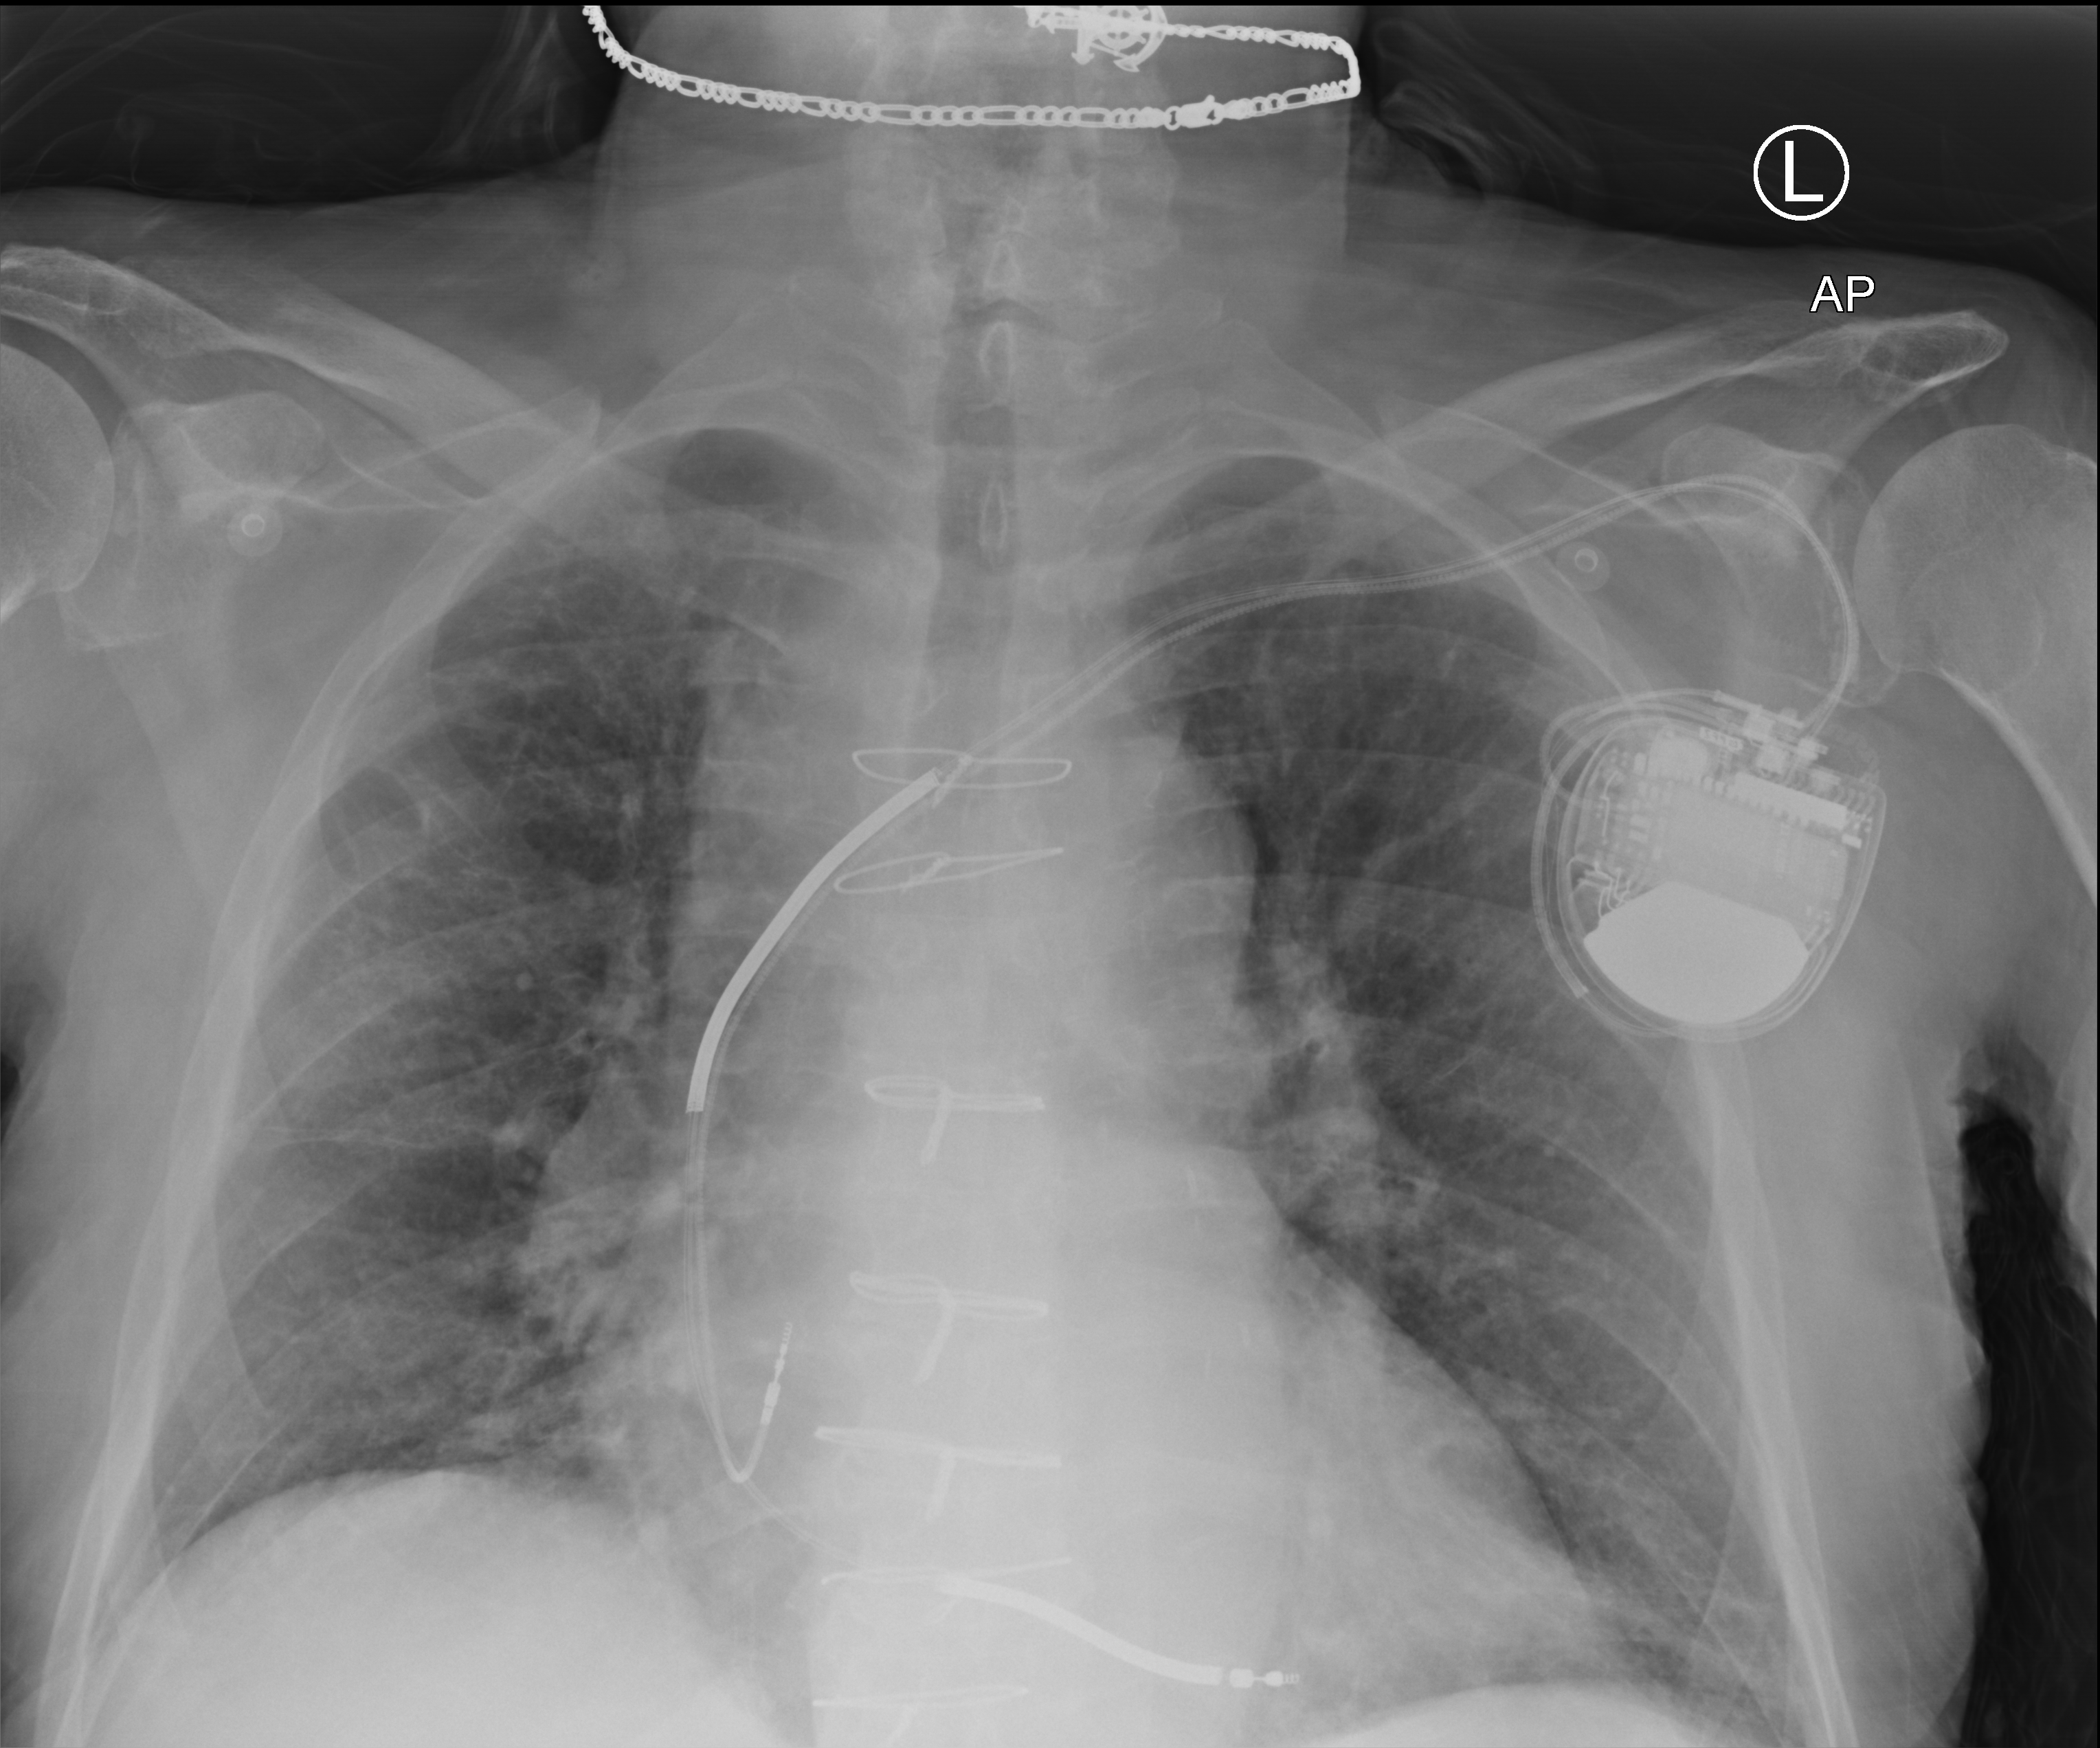
Chest X-ray (portable), anteroposterior (AP) projection. Male patient hospitalised with COVID-19, age 75–90 years.
From the hospital-stay record, not from the radiograph (when in the stay this image was taken is not recorded): mechanically ventilated during this hospital stay: no; other chronic lung disease (admission record): no.